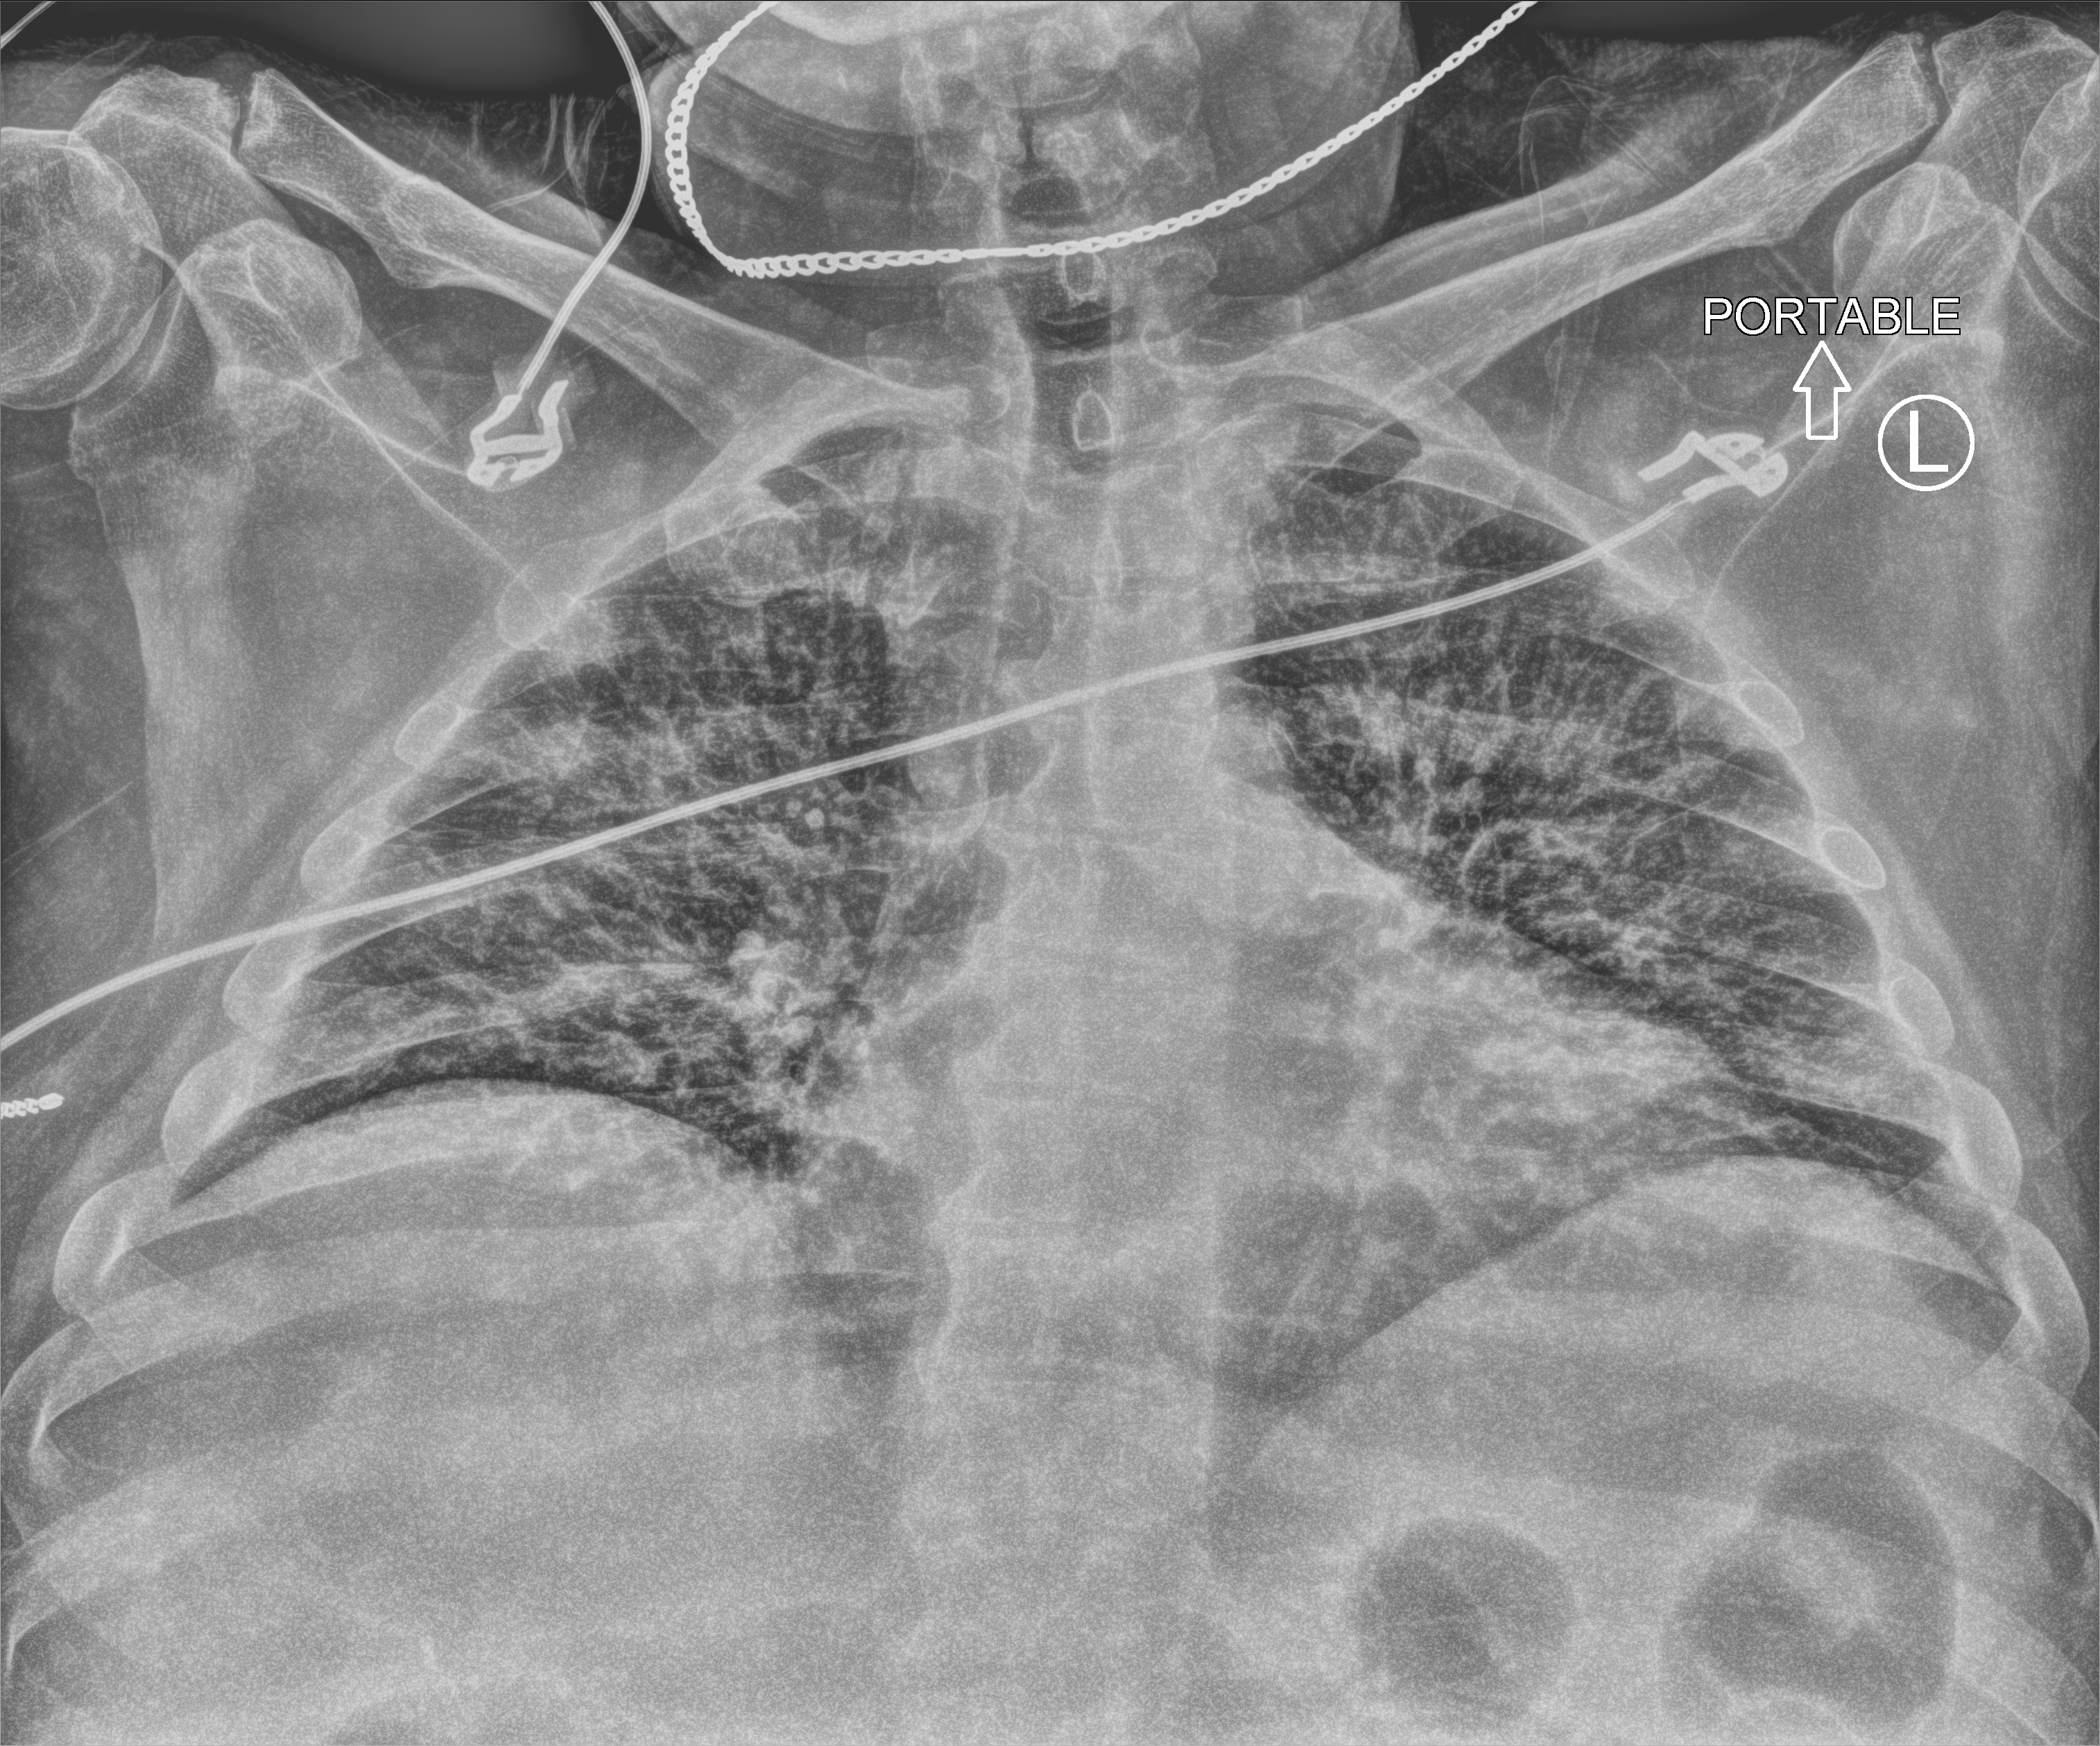
Portable chest radiograph, anteroposterior (AP) projection. Male patient hospitalised with COVID-19, age 18–59 years.
Admission-level facts for this patient (not findings on this image; timing relative to this image not recorded): hypertension (admission record): yes; admitted to intensive care during this hospital stay: no.